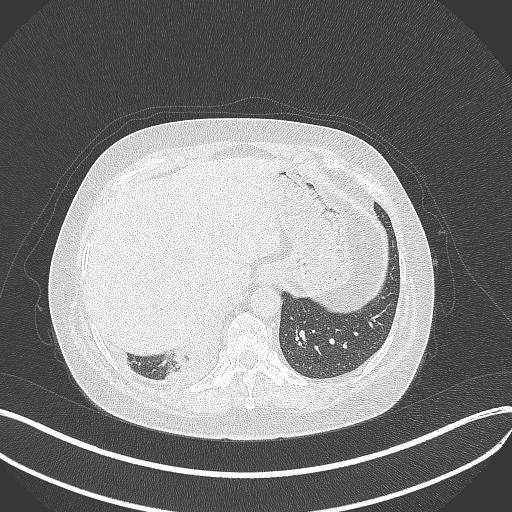
Chest CT, one axial slice. Position 71 of 381 along the scan axis. 120 kVp. Lung window (W 1500 / L -600 HU). 1 mm slice thickness. 512 × 512 image matrix. Female patient, age 56 years. Case-level facts recorded for this patient, not image findings: clinical TNM (as recorded): T2b N1 M0; histopathological grade: G3.
Structures marked on this image (bounding box drawn by a radiologist):
- lung tumour (recorded histology: small cell carcinoma): bounding box <169,343,194,371> (left, top, right, bottom; pixels)